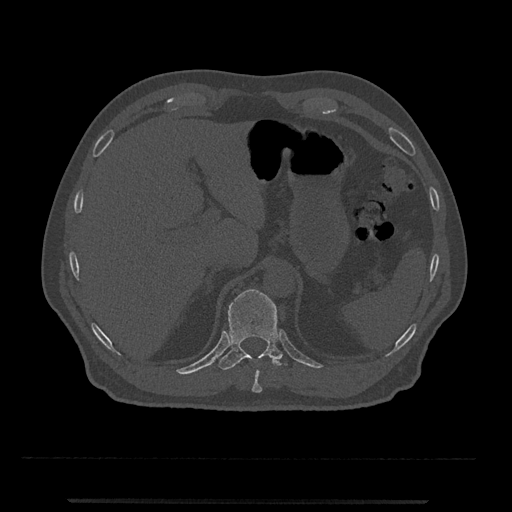
CT including the spine, one axial slice; slice 478 of 797 in the series (ordered by position); reconstruction kernel Br40s/3; 120 kVp; bone window (W 1800 / L 400 HU); 0.5 mm slice thickness; 512 × 512 image matrix. Patient: male, 63 years. From the clinical record (not read from this slice): primary cancer: prostate.
Annotated regions visible in this slice (semi-automatically segmented with operator editing):
- T10 vertebra: bounding box <252,358,272,393> (left, top, right, bottom; pixels)
- T11 vertebra: <218,289,287,370>